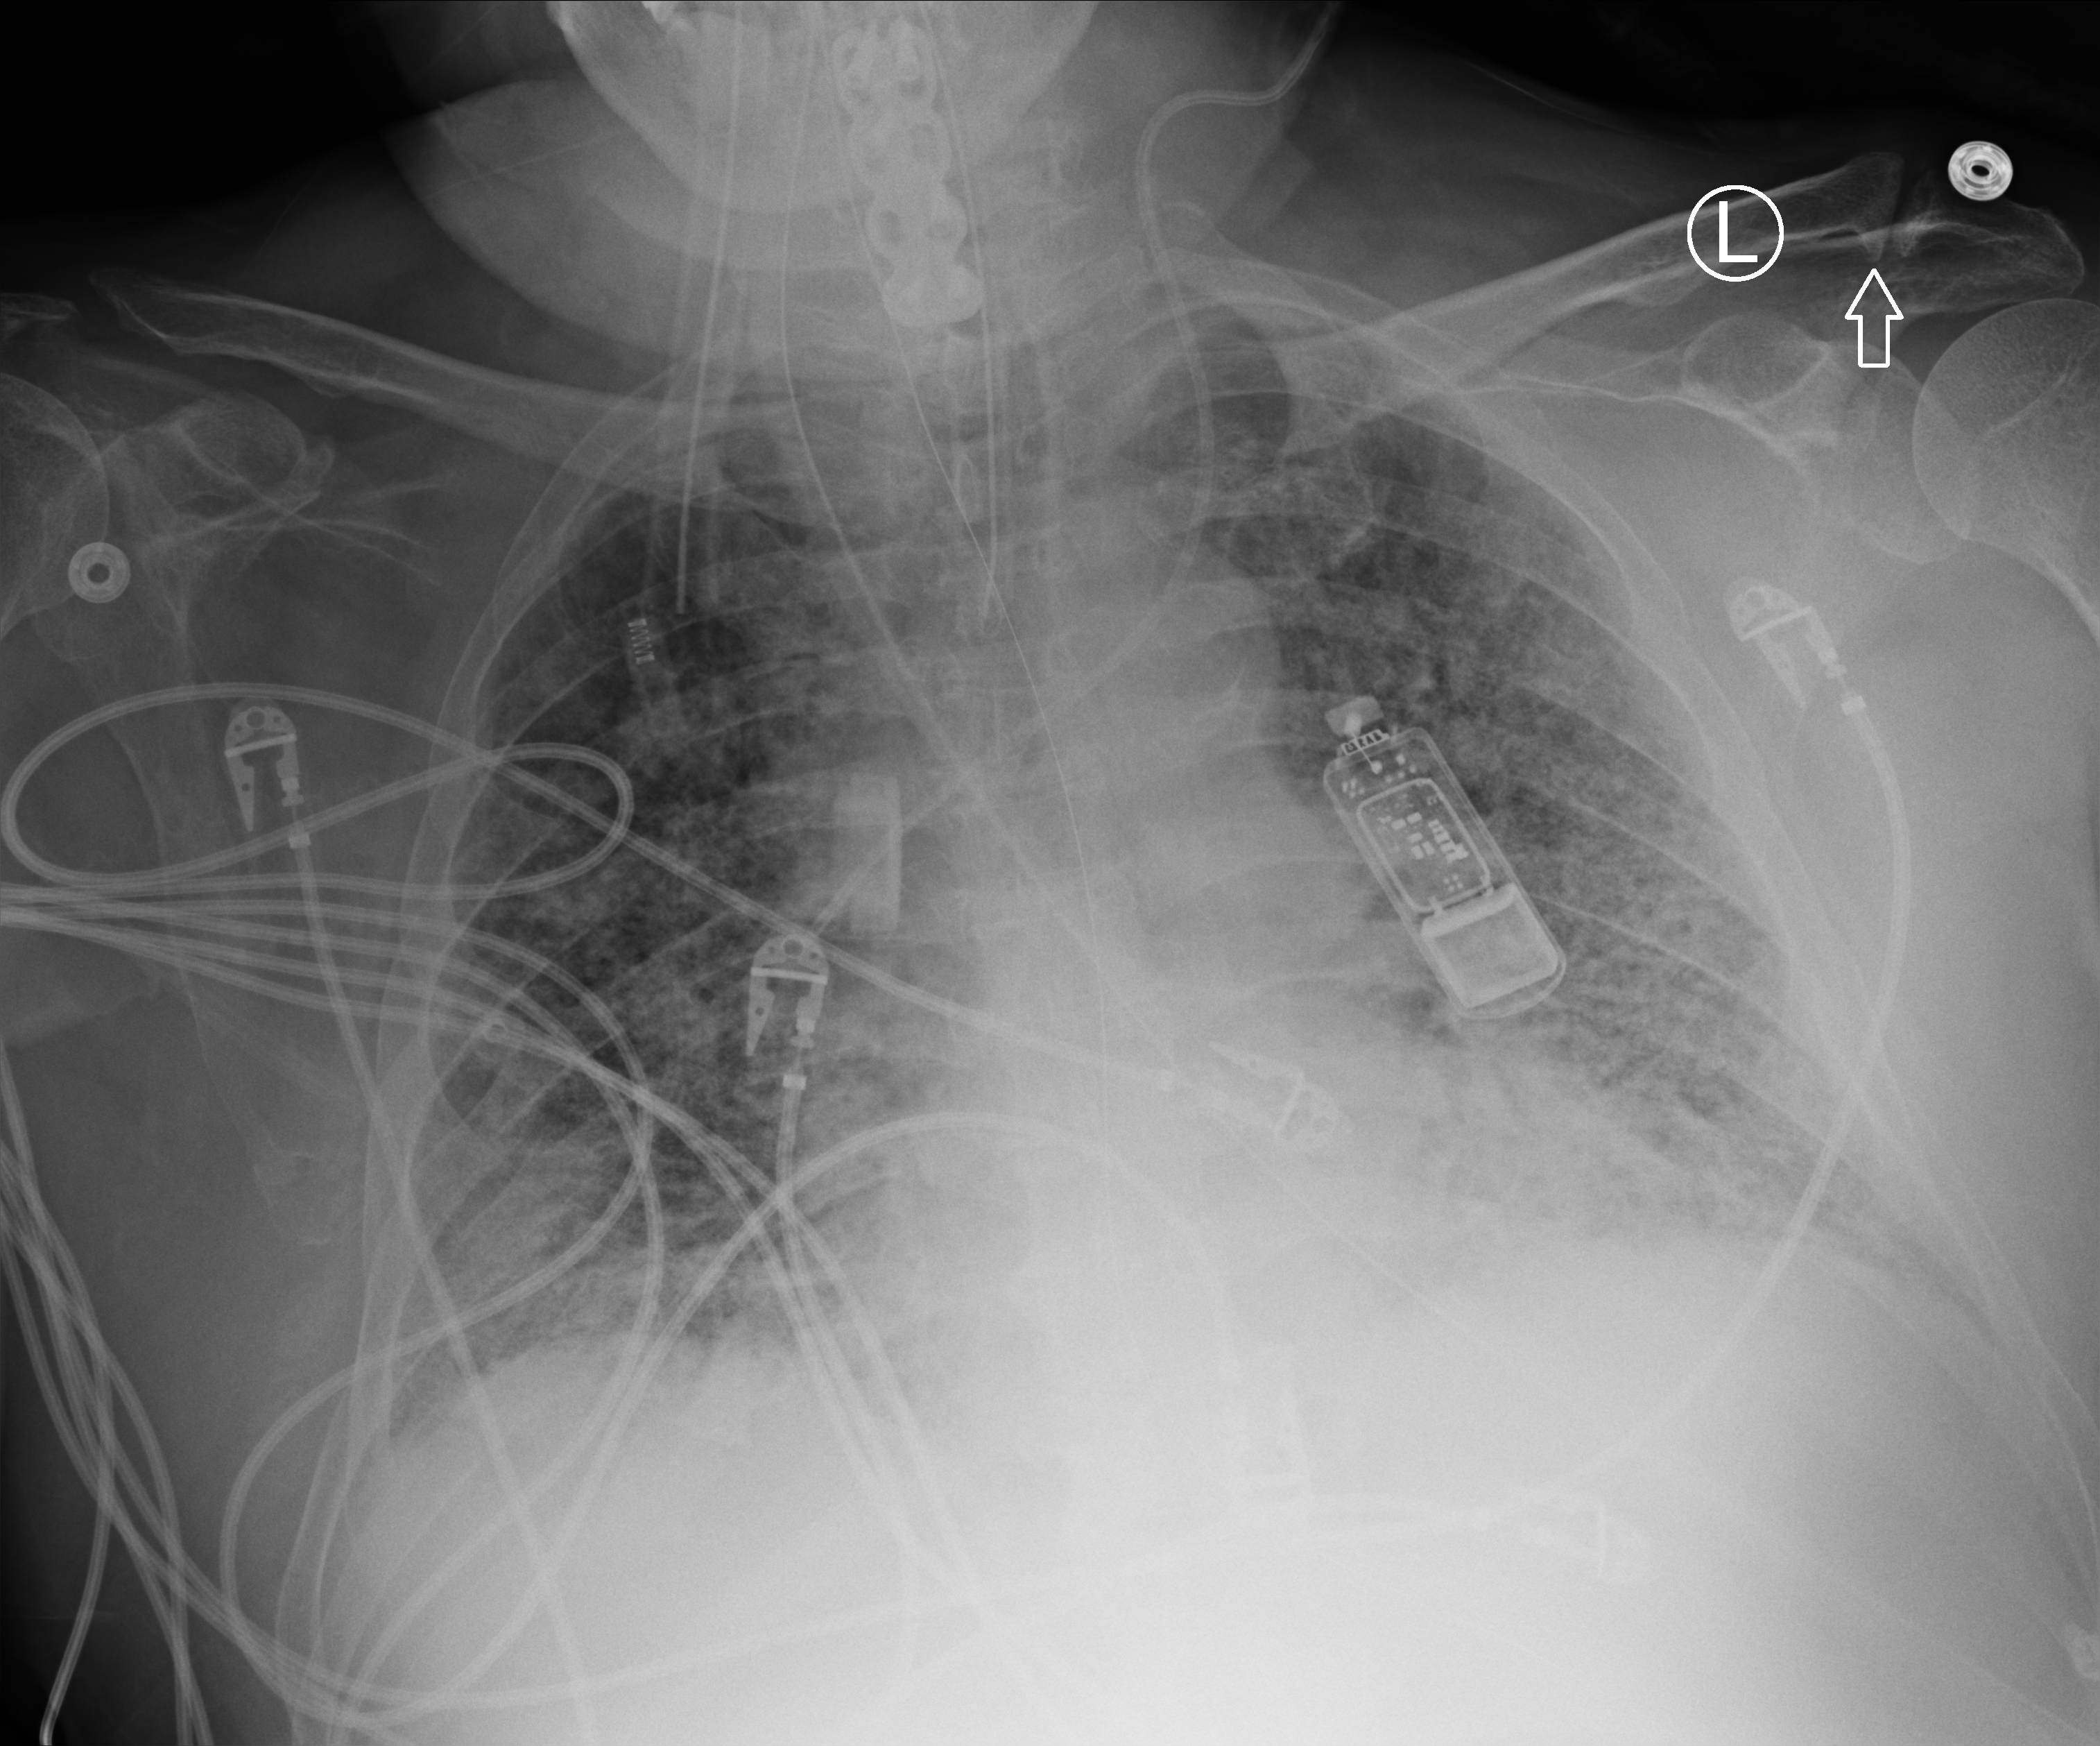
Portable chest radiograph. Patient hospitalised with COVID-19; male, aged 60–74 years.
From the hospital-stay record, not from the radiograph (when in the stay this image was taken is not recorded):
- mechanically ventilated during this hospital stay: yes
- length of hospital stay: 7 days
- admitted to intensive care during this hospital stay: yes